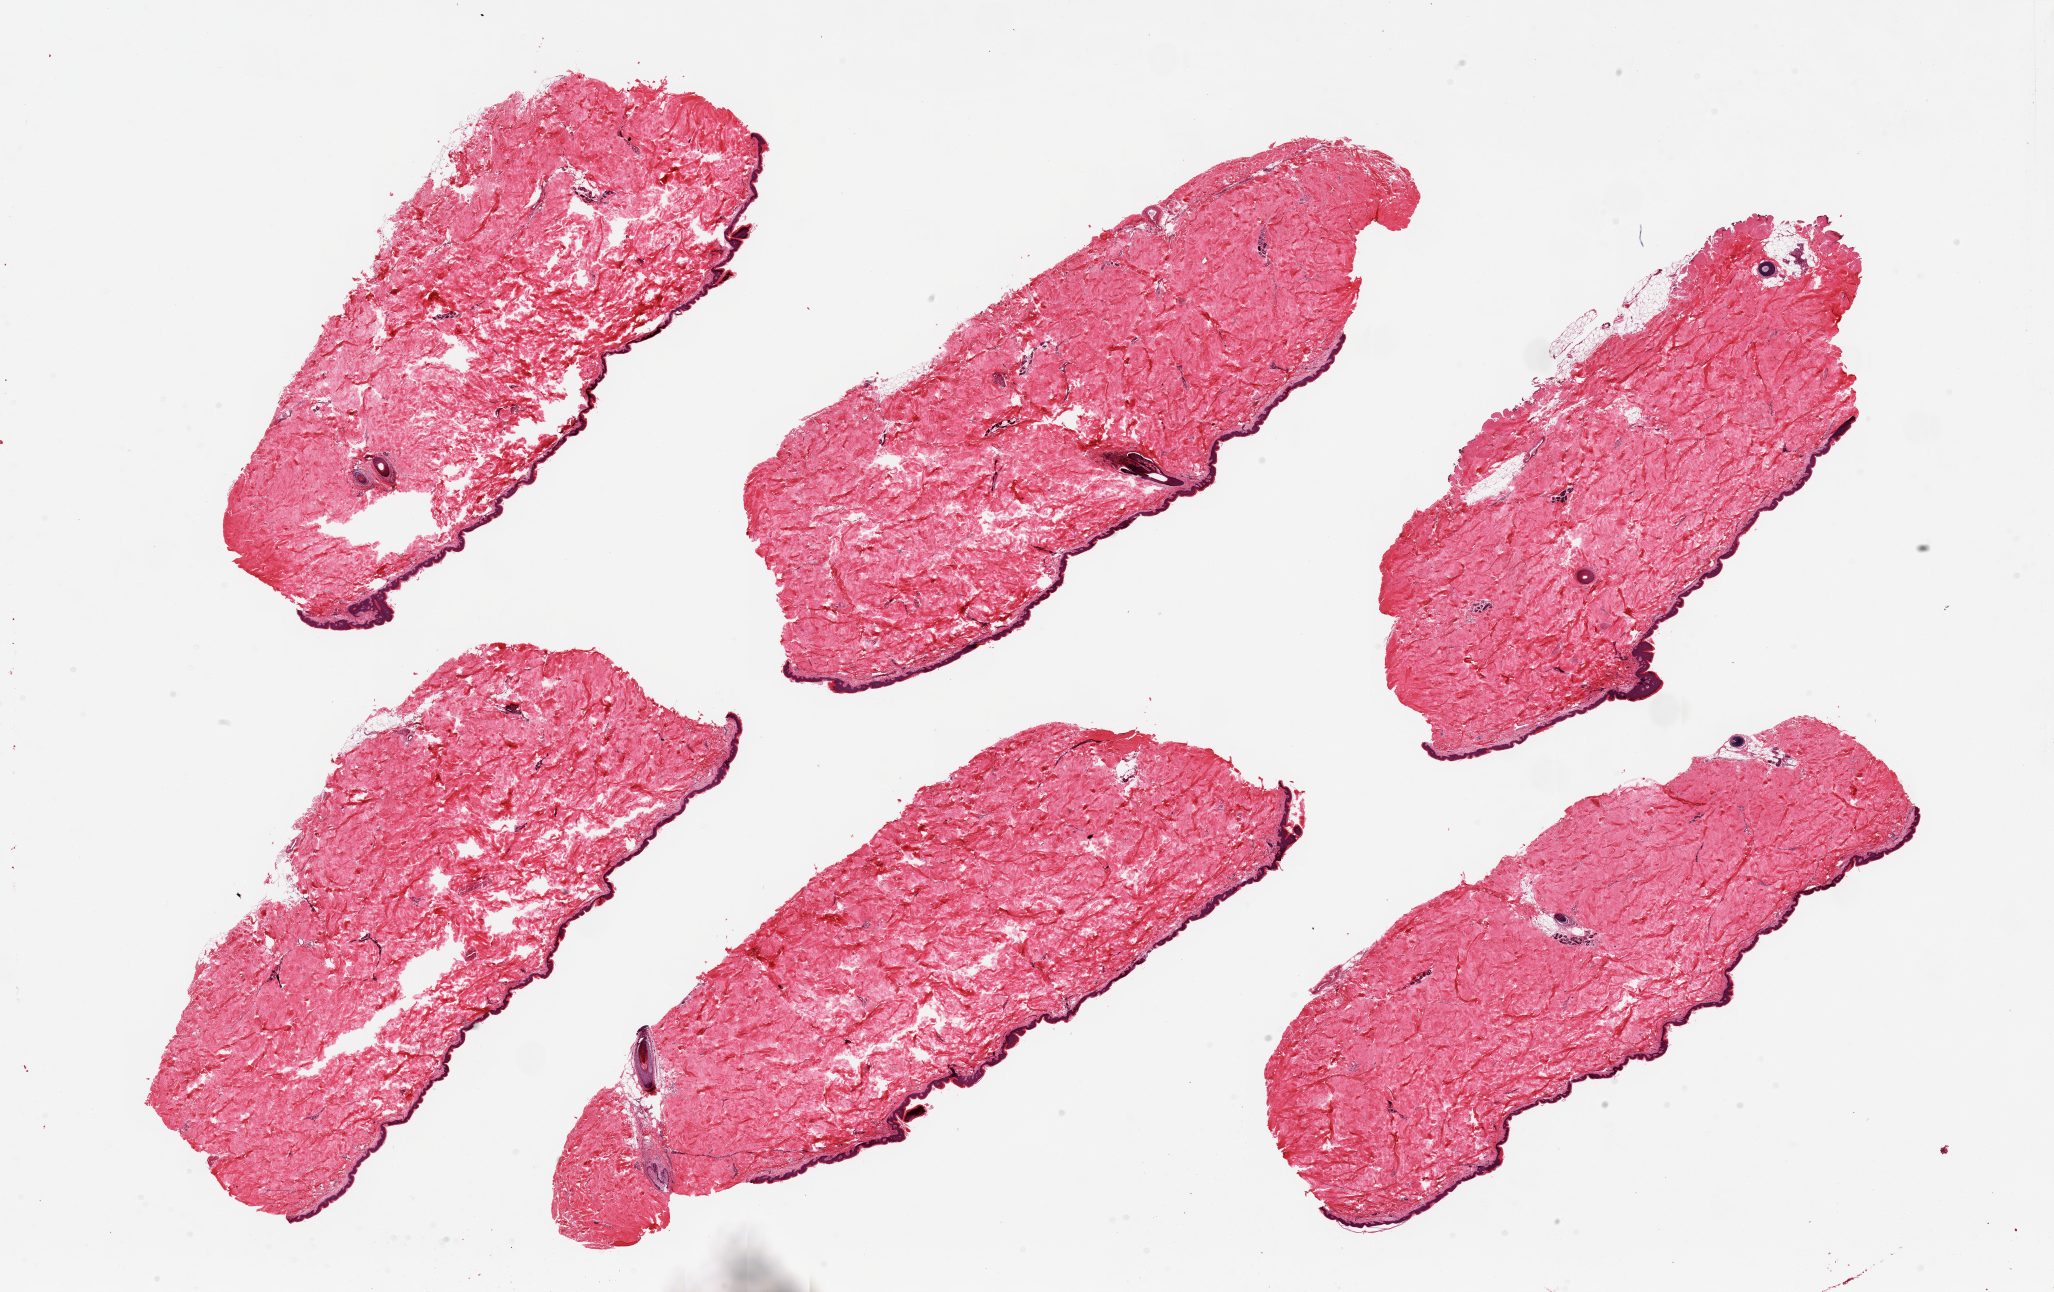
Digitized haematoxylin and eosin-stained section — shown as a low-resolution overview of the whole scanned area (about 32.5 x 20.4 mm, from a 20x scan); PAXgene-fixed, paraffin-embedded tissue; target tissue: skin of suprapubic region; tissue donor sample. Donor sex: male.
• reviewer comment on this tissue sample: 6 pieces; well trimmed